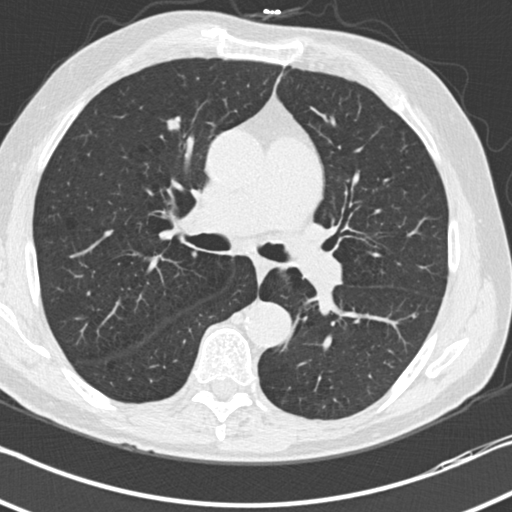
Chest CT (low-dose screening protocol), one axial image; third screening round (two years after baseline); lung window (W 1500 / L -600 HU); standard (soft-tissue) reconstruction kernel (B30f); 120 kVp; 512 × 512 image matrix, field of view 336 × 336 mm. Male, age 70 years at enrolment. Current smoker at enrolment.
Expert-annotated lung lesion, bounding box (x1, y1, x2, y2) in pixels: (155, 109, 194, 142). Reader record for this screening exam (exam-level; its link to the box is not recorded): non-calcified nodule or mass ≥4 mm, right middle lobe, 9 × 8 mm, smooth margins, soft tissue attenuation, pre-existing on the prior screen: no. Later outcome: lung cancer diagnosed 53 days after this screen — squamous cell carcinoma, NOS, right upper lobe, moderately differentiated (G2), stage IA (AJCC 6th edition), 10 mm at pathology.